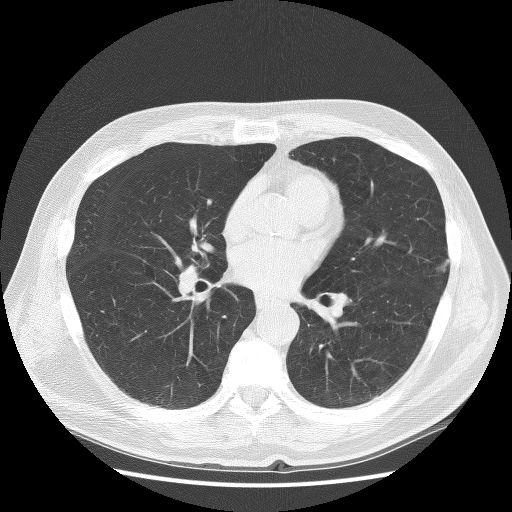
Axial slice from a low-dose chest CT screening exam; baseline screening round; lung window (W 1500 / L -600 HU); lung (sharp) reconstruction kernel (BONE); 120 kVp; slice 126 of 272 in the series; 512 × 512 image matrix. Male participant, aged 67 years at enrolment.
- Expert-annotated lung lesion, bounding box (x1, y1, x2, y2) in pixels: (402, 242, 464, 296).
- Screening reader's record for this exam: no non-calcified nodule ≥4 mm recorded.
- Later outcome: lung cancer diagnosed 772 days after this screen — squamous cell carcinoma, NOS, left upper lobe, moderately differentiated (G2), stage IB (AJCC 6th edition), 25 mm at pathology.